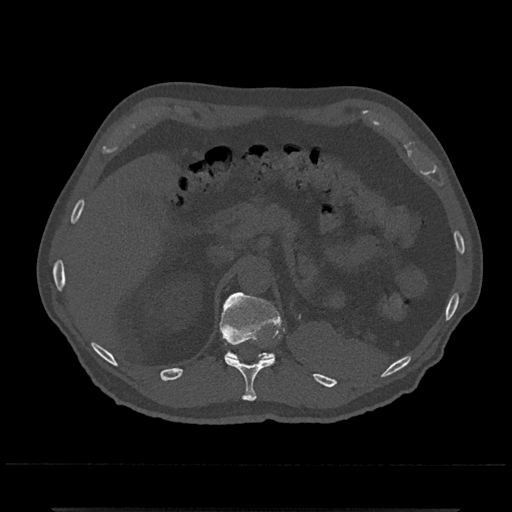
CT including the spine, one axial slice; slice 464 of 797 in the series (ordered by position); reconstruction kernel Br40s/3; bone window (W 1800 / L 400 HU); 0.5 mm slice thickness; 512 × 512 image matrix. Male patient, age 67 years. Case-level facts recorded for this patient, not image findings: primary cancer: prostate.
Outlined on this slice (semi-automatically segmented with operator editing):
- T11 vertebra: bounding box <225,342,275,401> (left, top, right, bottom; pixels)
- T12 vertebra: <220,292,284,361>